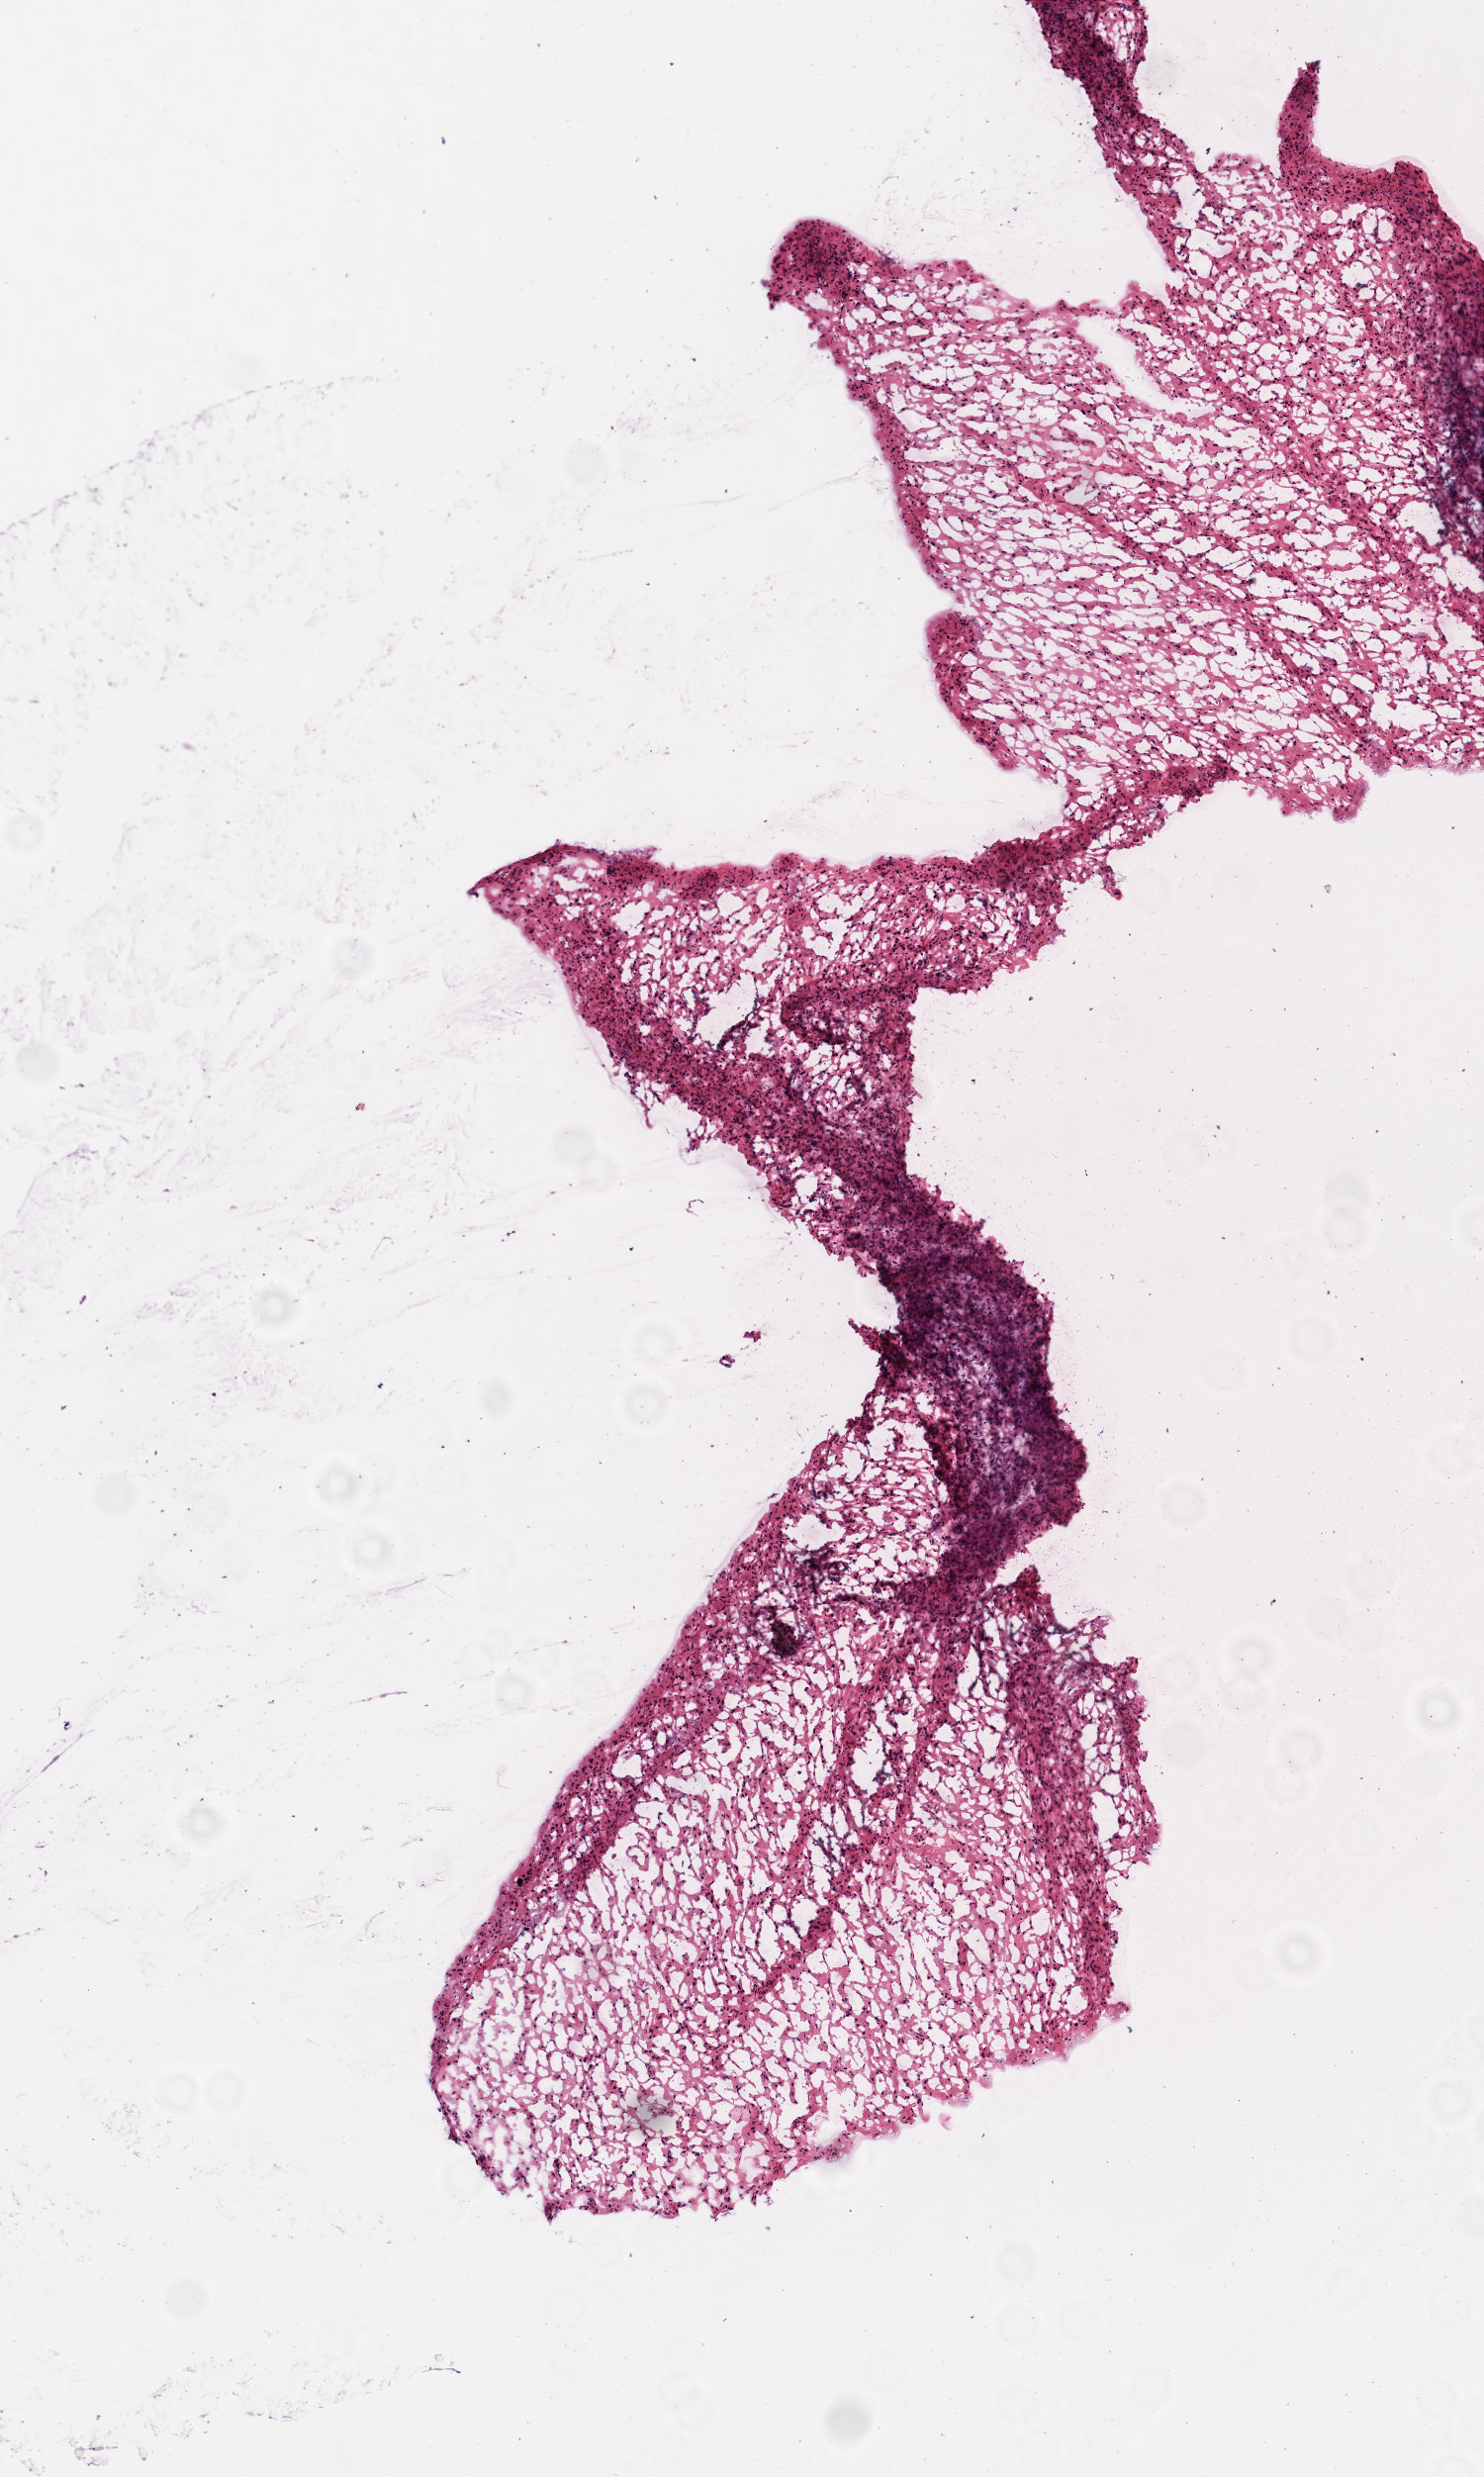
Whole-slide histology image, H&E, low-resolution overview of the scanned area, about 3.0 x 5.0 mm (slide scanned at 20x); frozen section from the top of the tissue portion; sample: primary tumour, brain. Patient: male, age at initial diagnosis 43 years. Pathologist review of this section (percent, as recorded): tumour cells 70%, tumour nuclei 65%, normal cells 10%, stromal cells 30%, necrosis 0%.
Histologic diagnosis: Glioblastoma.